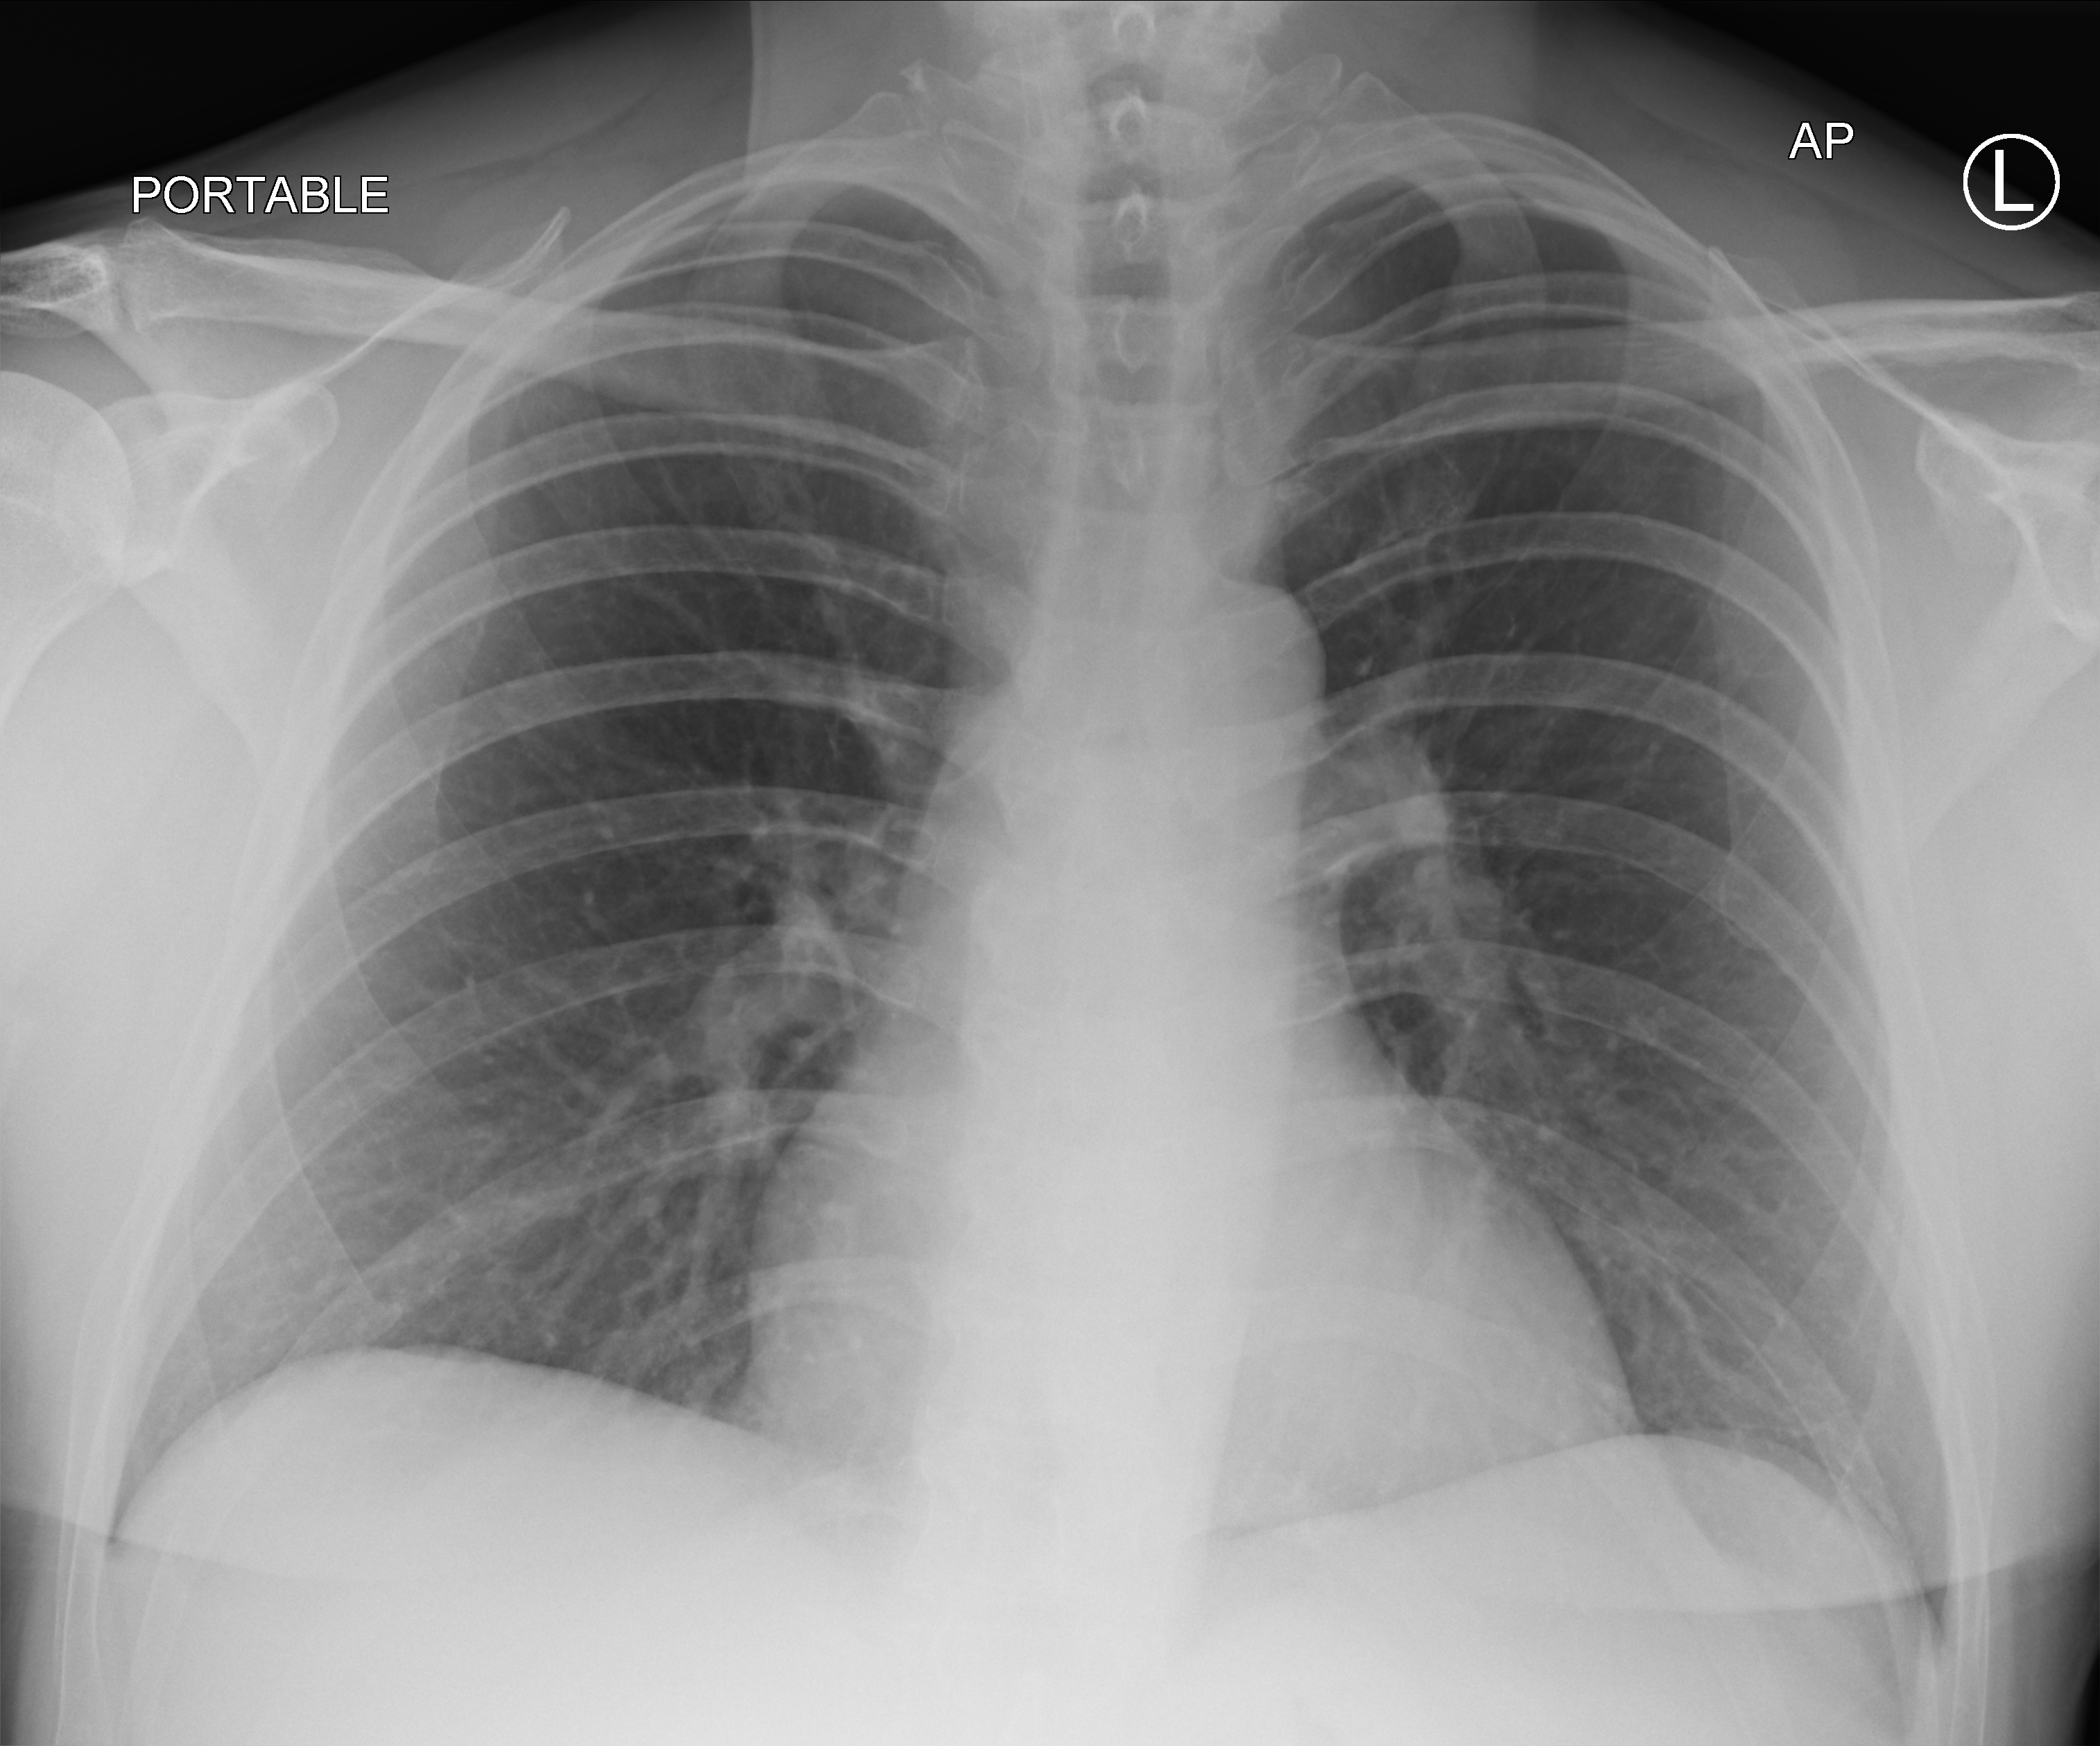
Bedside chest radiograph (computed radiography). Male patient hospitalised with COVID-19, age 18–59 years.
Admission-level facts for this patient (not findings on this image; timing relative to this image not recorded): chronic kidney disease (admission record): no; diabetes (admission record): no; admitted to intensive care during this hospital stay: no.